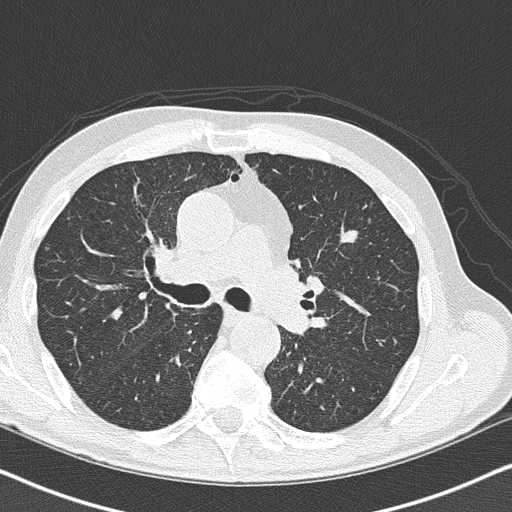
Low-dose screening chest CT, one axial slice; slice 99 of 158 in the series (ordered by position); 120 kVp; lung window (W 1500 / L -600 HU); 2 mm slice thickness; 512 × 512 image matrix, field of view 330 × 330 mm.
Outlined on this slice (expert manual segmentation):
- lesion 1 (tumor, upper lobe of left lung): box from (x=342, y=231) to (x=357, y=243) px